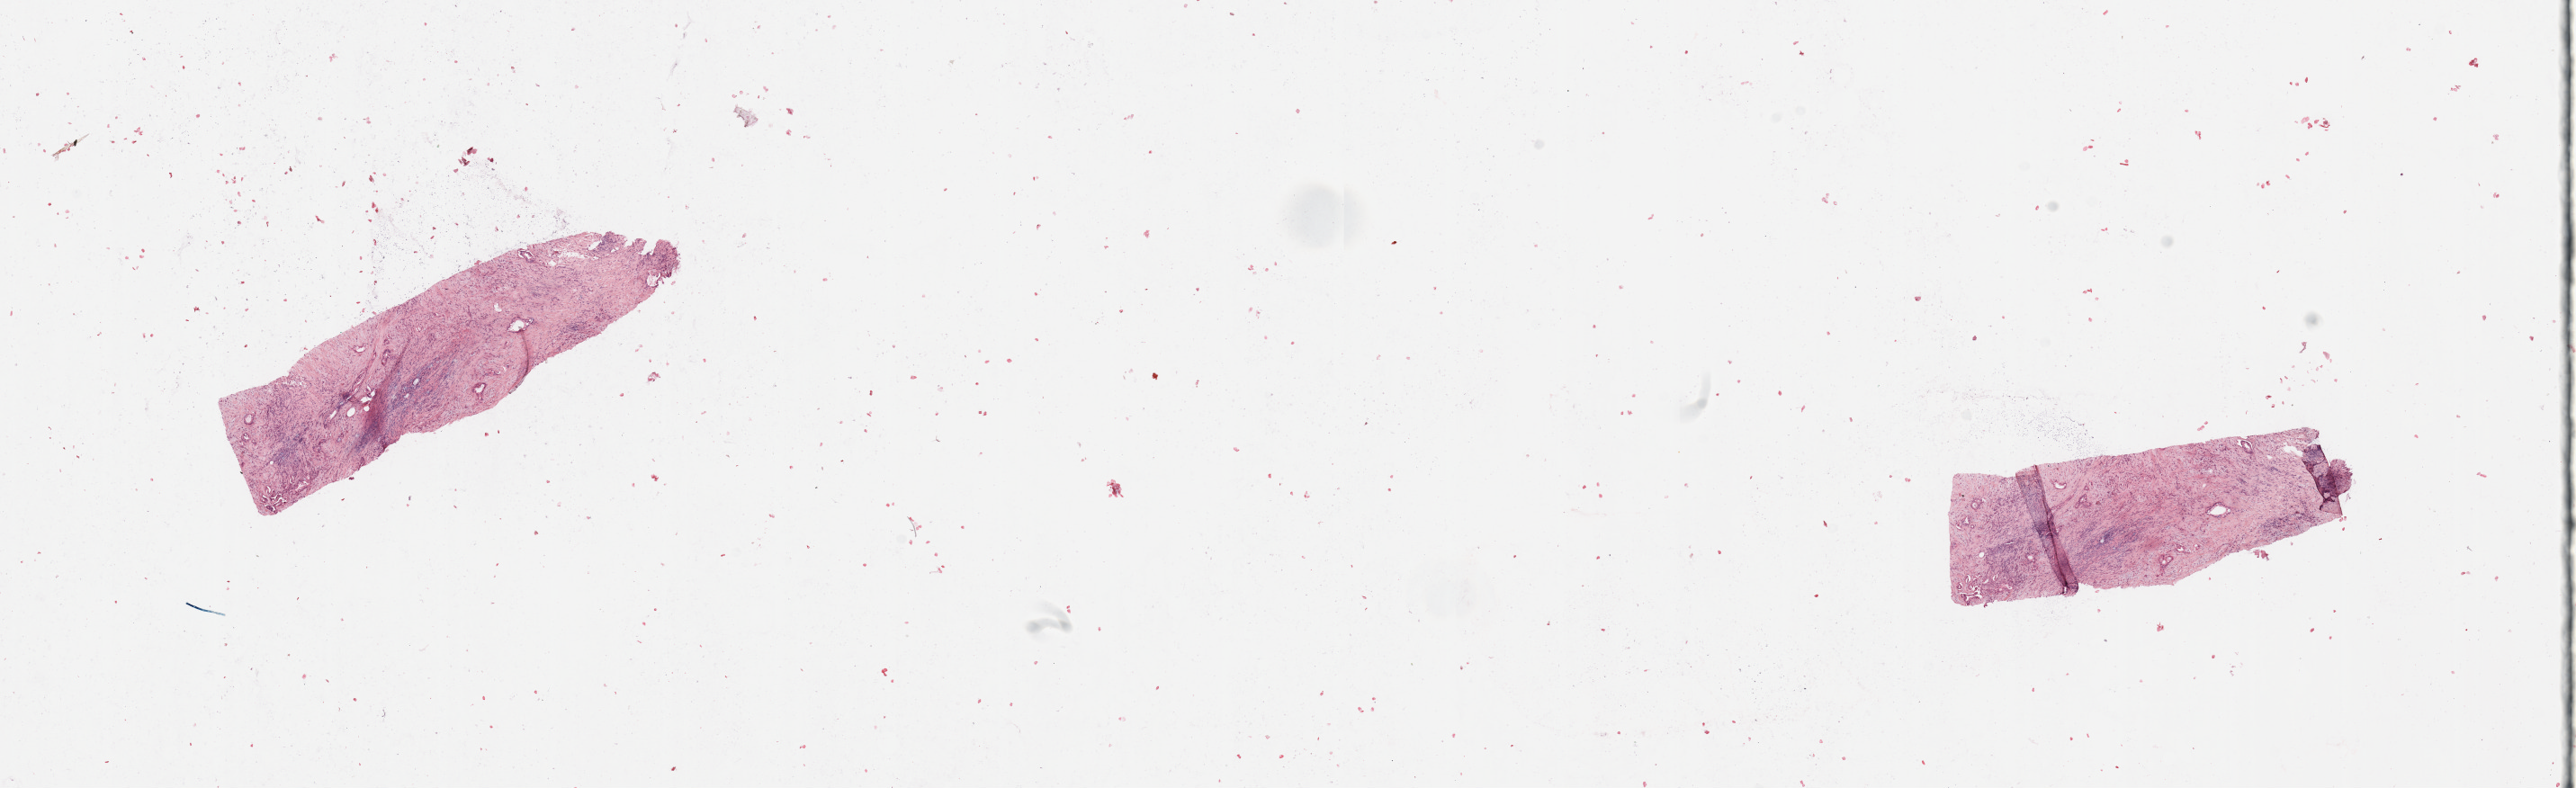
Whole-slide histology image, H&E — low-resolution overview of the scanned area, about 22.6 x 6.9 mm (from a 20x scan). Tumour tissue sample, sampled site: pancreas. Patient: male, age 42 years. Histologic grade: G2 (moderately differentiated). Pathologist review of this section (percent, as recorded): tumour nuclei 10%, necrosis 0%.
Primary tumour site (as recorded): head. Diagnosis: Infiltrating duct carcinoma, NOS. AJCC pathologic stage: IIB.